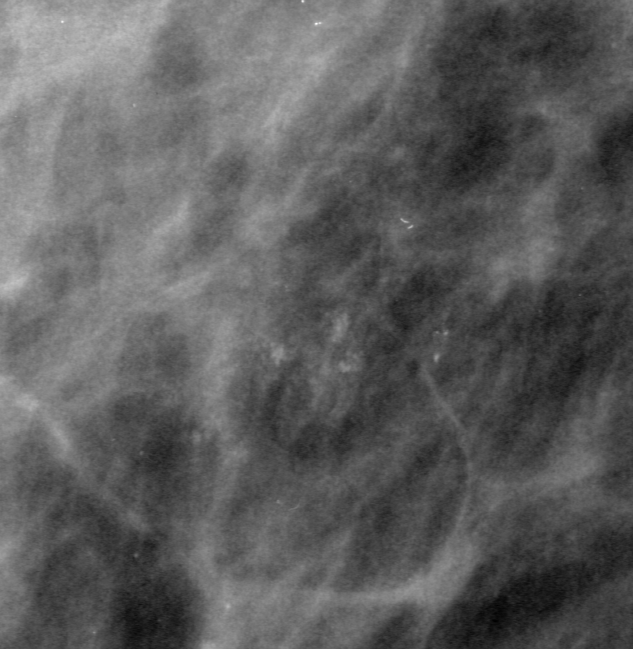
Region of interest cut from a scanned film mammogram (one marked finding), left breast, MLO view.
Finding: calcifications, morphology pleomorphic, distribution clustered; BI-RADS assessment category 4; pathology result (as recorded, not read from the image): benign.